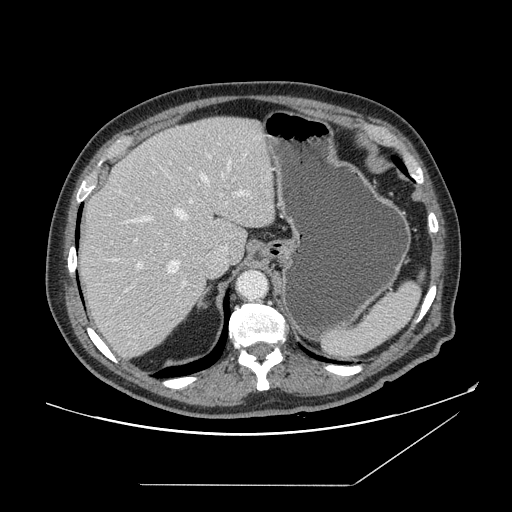
Contrast-enhanced abdominal CT, one axial slice. Slice 116 of 166 in the series (ordered by position). 120 kVp. Soft-tissue window (W 400 / L 40 HU). 2.5 mm slice thickness. 512 × 512 image matrix. Male patient, age 80 years. From the clinical record (not read from this slice): diagnosis: colorectal cancer liver metastases, imaged before liver resection; multiple liver metastases: no; largest metastasis: 2.2 cm; chemotherapy before resection: no.
Structures marked on this image (expert manual segmentation):
- hepatic veins: box from (x=125, y=161) to (x=231, y=274) px
- liver: (x=79, y=117)–(x=275, y=359)
- planned liver remnant (the part of the liver to remain after resection): (x=81, y=117)–(x=275, y=263)
- portal vein (with intrahepatic branches): (x=136, y=156)–(x=247, y=326)